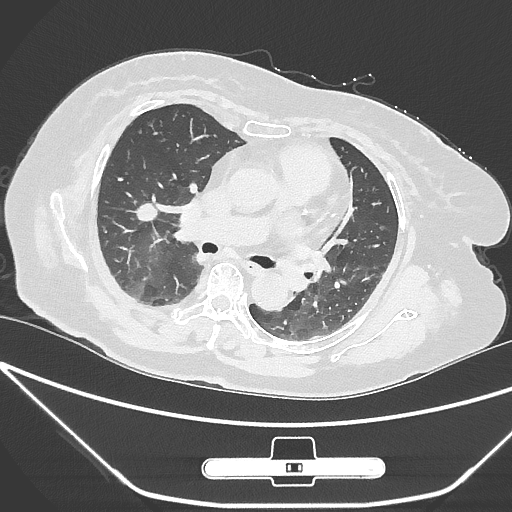
Chest CT, one axial slice. Slice 156 of 245 in the series (ordered by position). 120 kVp. Lung window (W 1500 / L -600 HU). 512 × 512 image matrix, field of view 365 × 365 mm. Female patient, age 65 years. From the clinical record (not read from this slice): clinical TNM (as recorded): T1c N0 M0.
Structures marked on this image (bounding box drawn by a radiologist):
- lung tumour (recorded histology: adenocarcinoma): box from (x=134, y=192) to (x=160, y=229) px